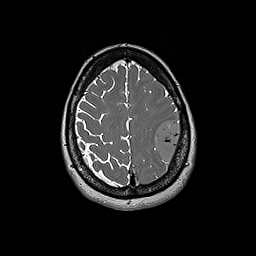
Brain MRI from a brain-tumour surgery series, one axial slice; slice 56 of 192 in the series (ordered by position); 1 mm slice thickness; 256 × 256 image matrix, field of view 250 × 250 mm. Case-level facts recorded for this patient, not image findings: histopathology: Glioblastoma; WHO grade: 4.
Outlined on this slice (outlined manually by an expert reader):
- tumour: bounding box (x1, y1, x2, y2) in pixels: (155, 120, 183, 166)